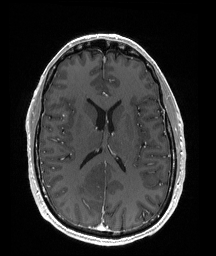
Brain MRI from a brain-tumour surgery series, one axial slice. Slice 81 of 176 in the series (ordered by position). T1-weighted post-contrast. 1 mm slice thickness. 216 × 256 image matrix. Case-level facts recorded for this patient, not image findings: histopathology: Oligodendroglioma; WHO grade: 2; IDH mutation: yes; tumour location: Right Parietal.
Structures marked on this image (expert manual segmentation):
- tumour: bounding box [x1, y1, x2, y2] px = [70, 166, 111, 196]